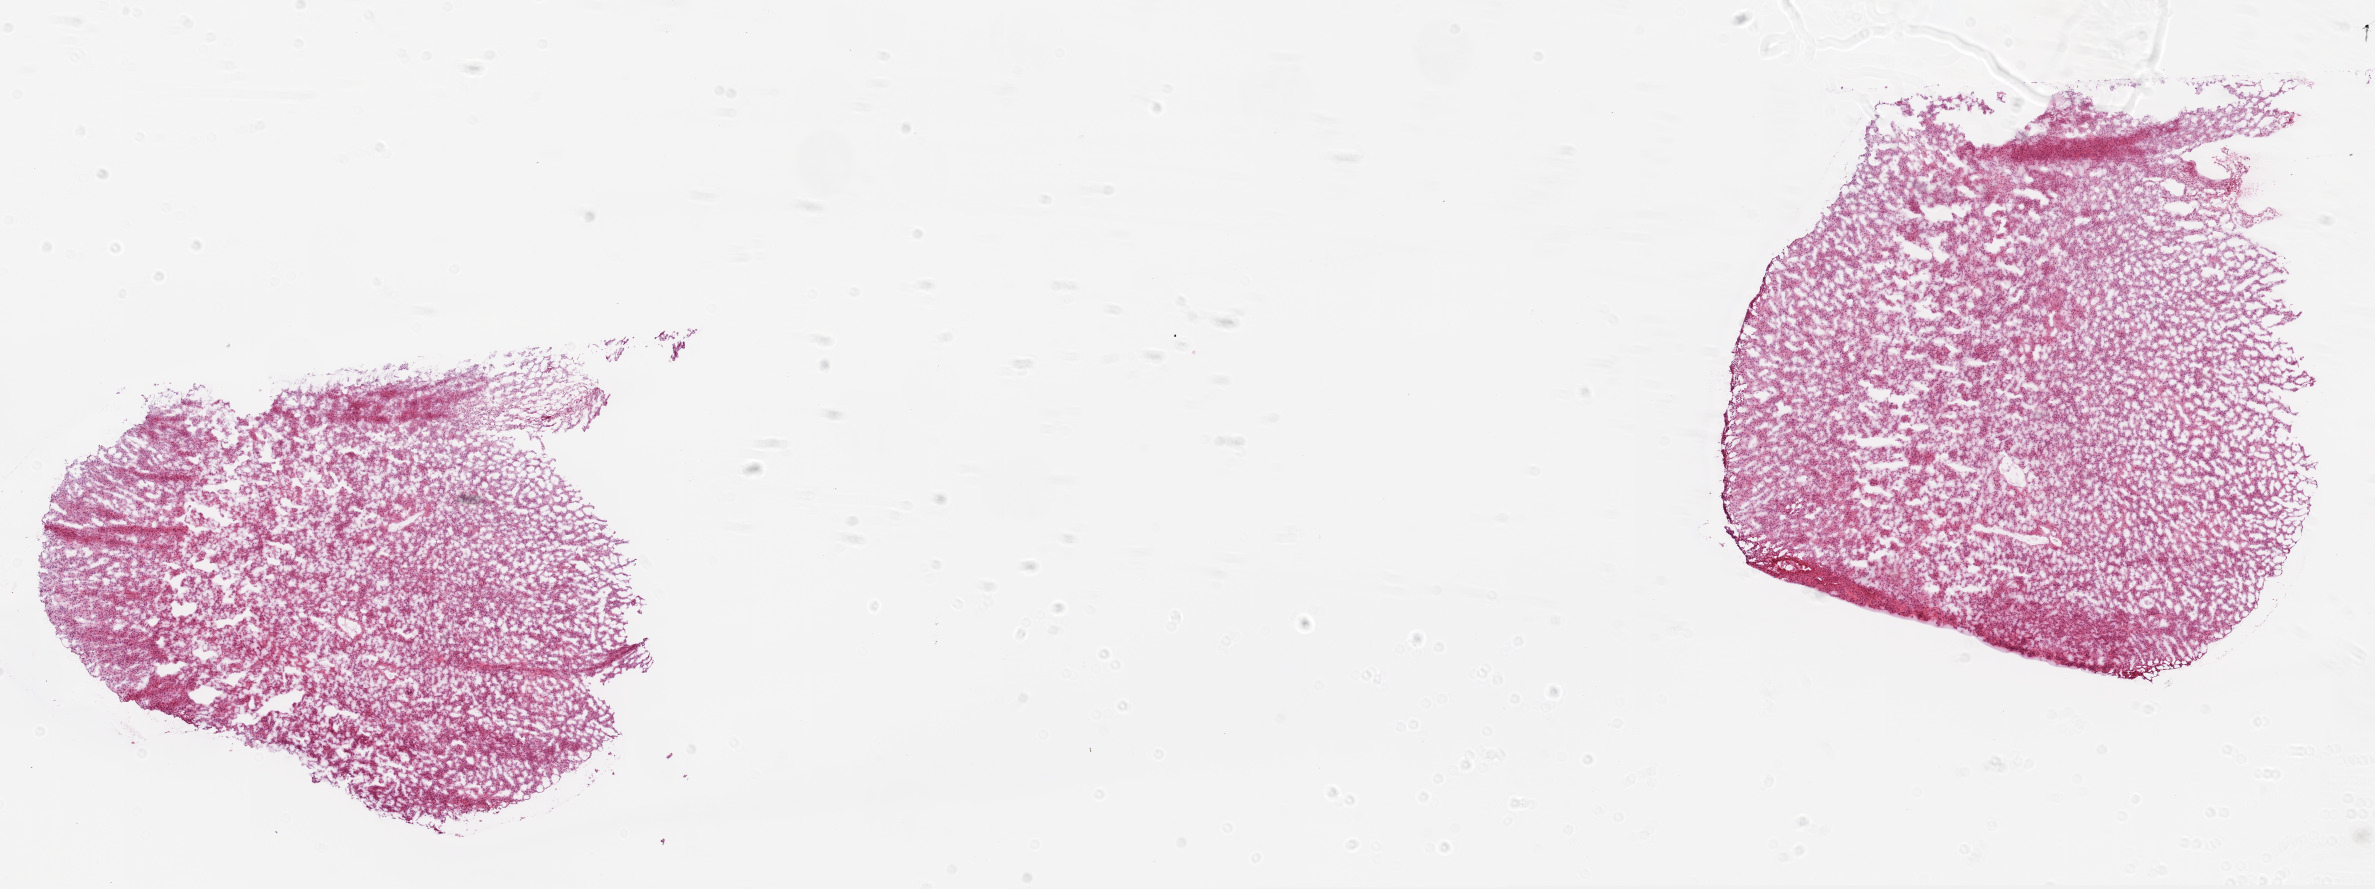
Hematoxylin and eosin (H&E) stained whole-slide image, a low-resolution overview of the entire scanned area, about 19.1 x 7.1 mm, frozen section from the top of the tissue portion, primary tumour sample from the brain. Female patient; age at initial diagnosis 67 years. Composition of this section per pathologist review: tumour cells 95%, tumour nuclei 95%, normal cells 0%, stromal cells 5%, necrosis 0%.
* histologic diagnosis: Glioblastoma